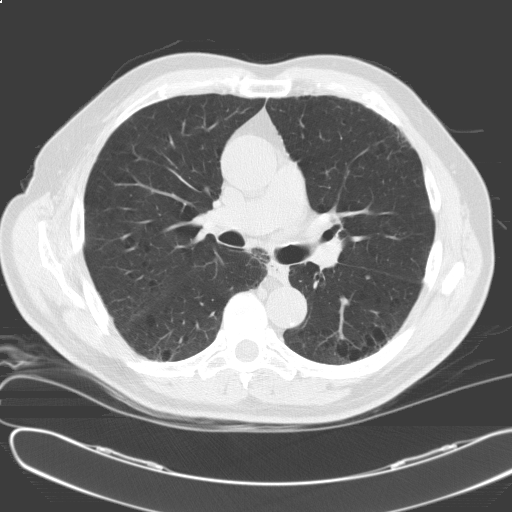
Low-dose screening chest CT, axial slice; baseline annual screen; lung window (W 1500 / L -600 HU); standard (soft-tissue) reconstruction kernel (C). Male participant, aged 69 years at enrolment. Former smoker at enrolment.
• Lesion marked by an expert reader, bounding box <154,138,188,169> (left, top, right, bottom; pixels).
• The screening reader recorded 2 non-calcified nodules or masses ≥4 mm on this exam (left upper lobe, right lower lobe); which of them this box marks is not recorded.
• Later outcome: lung cancer diagnosed 450 days after this screen (after the second annual screen) — adenosquamous carcinoma, right upper lobe, poorly differentiated (G3), stage IV (AJCC 6th edition), 30 mm at pathology.